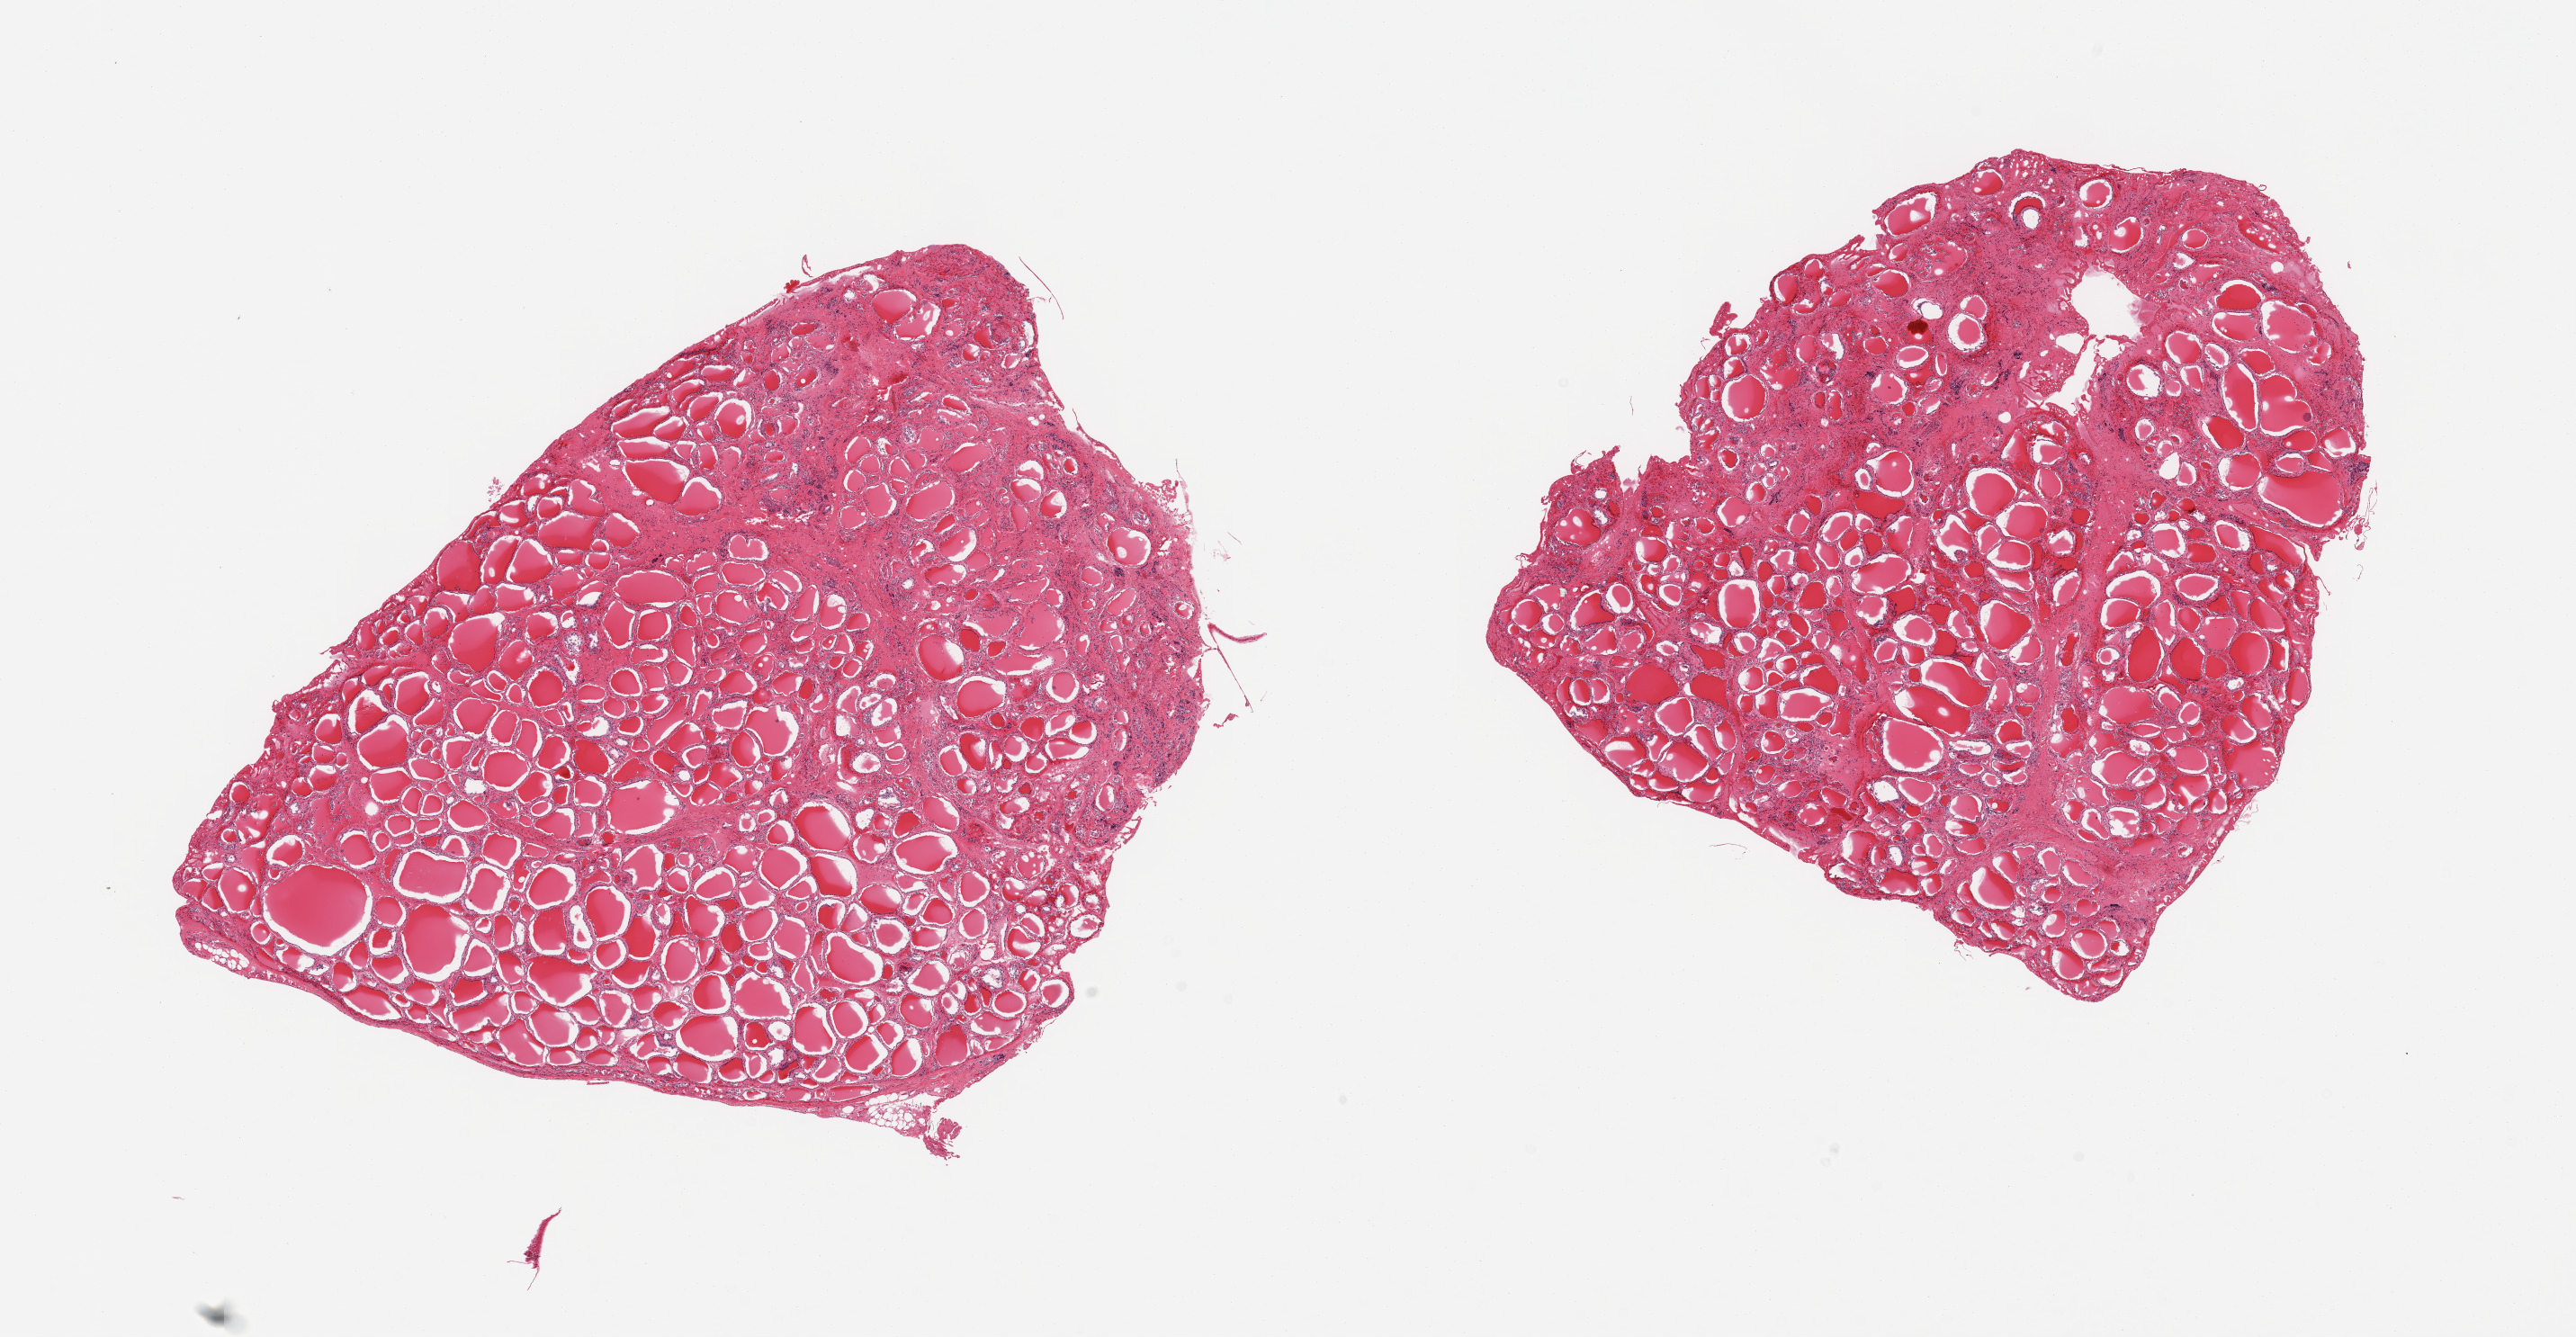
Whole-slide image, hematoxylin and eosin (H&E) stain, shown as a low-resolution overview of the whole scanned area (about 22.6 x 11.8 mm). PAXgene-fixed paraffin-embedded (PFPE) section. Target tissue: thyroid. Tissue donor sample. Donor: female.
Review note (as recorded): 2 pieces; well dissected.